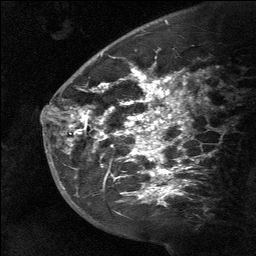
Breast MRI (dynamic contrast-enhanced), one sagittal slice. Position 43 of 64 along the scan axis. Dynamic contrast-enhanced study with each time point stored as its own series, time point 2 of 3 at this slice position (early post-contrast, ordered by acquisition time). 1.5 T. TE 4.8 ms, TR 27 ms. 256 × 256 image matrix, field of view 180 × 180 mm. Patient: female, 39 years. Case-level facts recorded for this patient, not image findings: setting: breast cancer imaged before/during neoadjuvant chemotherapy; receptor status: HER2-positive.
Structures marked on this image (semi-automatically segmented with operator editing):
- analysis volume of interest (the breast-tissue region the enhancement analysis was run in; not a lesion): bounding box <58,40,199,217> (left, top, right, bottom; pixels)
- tumour enhancement mask (voxels above the 90 % enhancement threshold inside the analysis volume of interest): <70,70,181,199>